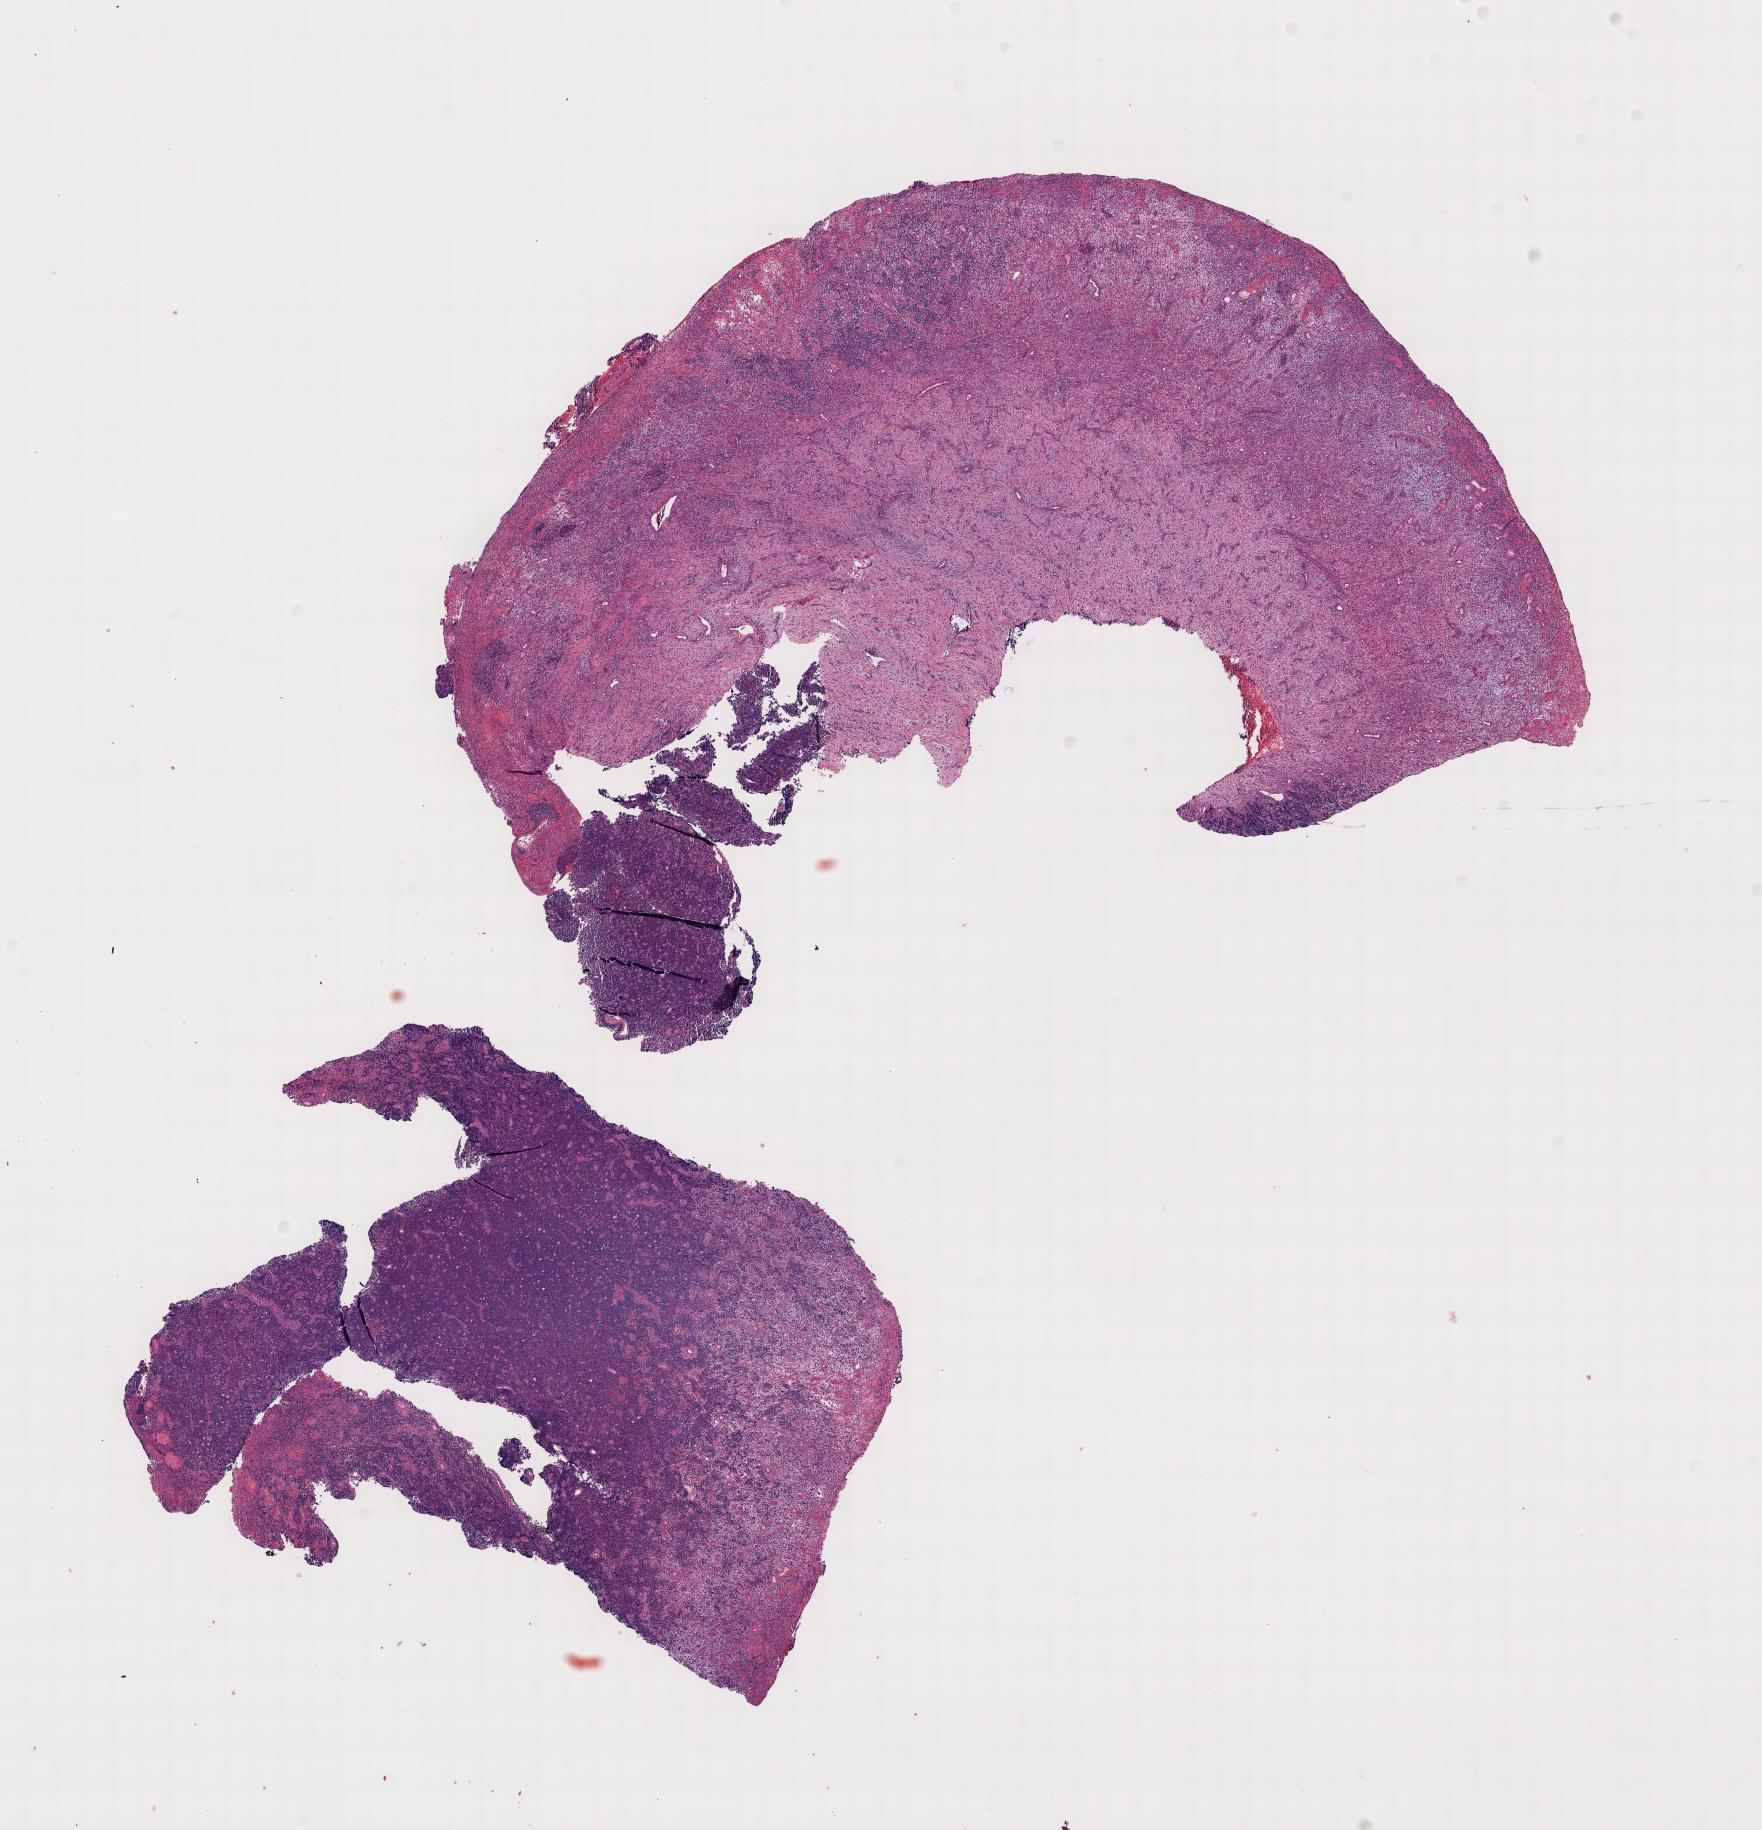
Hematoxylin and eosin (H&E) whole-slide image, shown as a low-resolution overview of the whole scanned area. Specimen: tumor tissue. Site: cranium. Patient: female, aged 11.
Histologic diagnosis: Burkitt lymphoma, NOS.